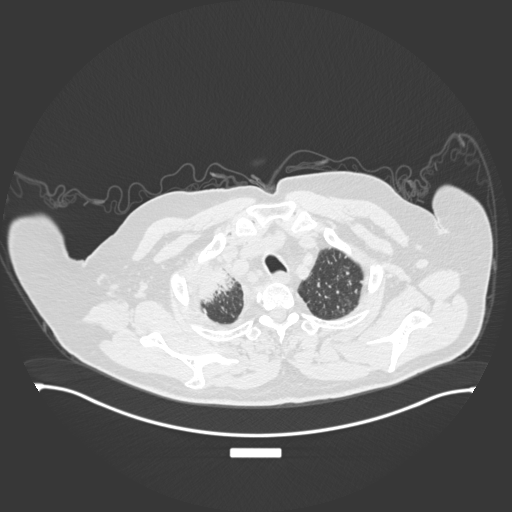
Chest CT, one axial slice. Position 172 of 201 along the scan axis. 120 kVp. Lung window (W 1500 / L -600 HU). 512 × 512 image matrix. Patient: male, 69 years. From the clinical record (not read from this slice): clinical TNM (as recorded): T4 N3 M1.
Structures marked on this image (bounding box drawn by a radiologist):
- lung tumour (recorded histology: adenocarcinoma): bounding box (x1, y1, x2, y2) in pixels: (196, 261, 248, 311)